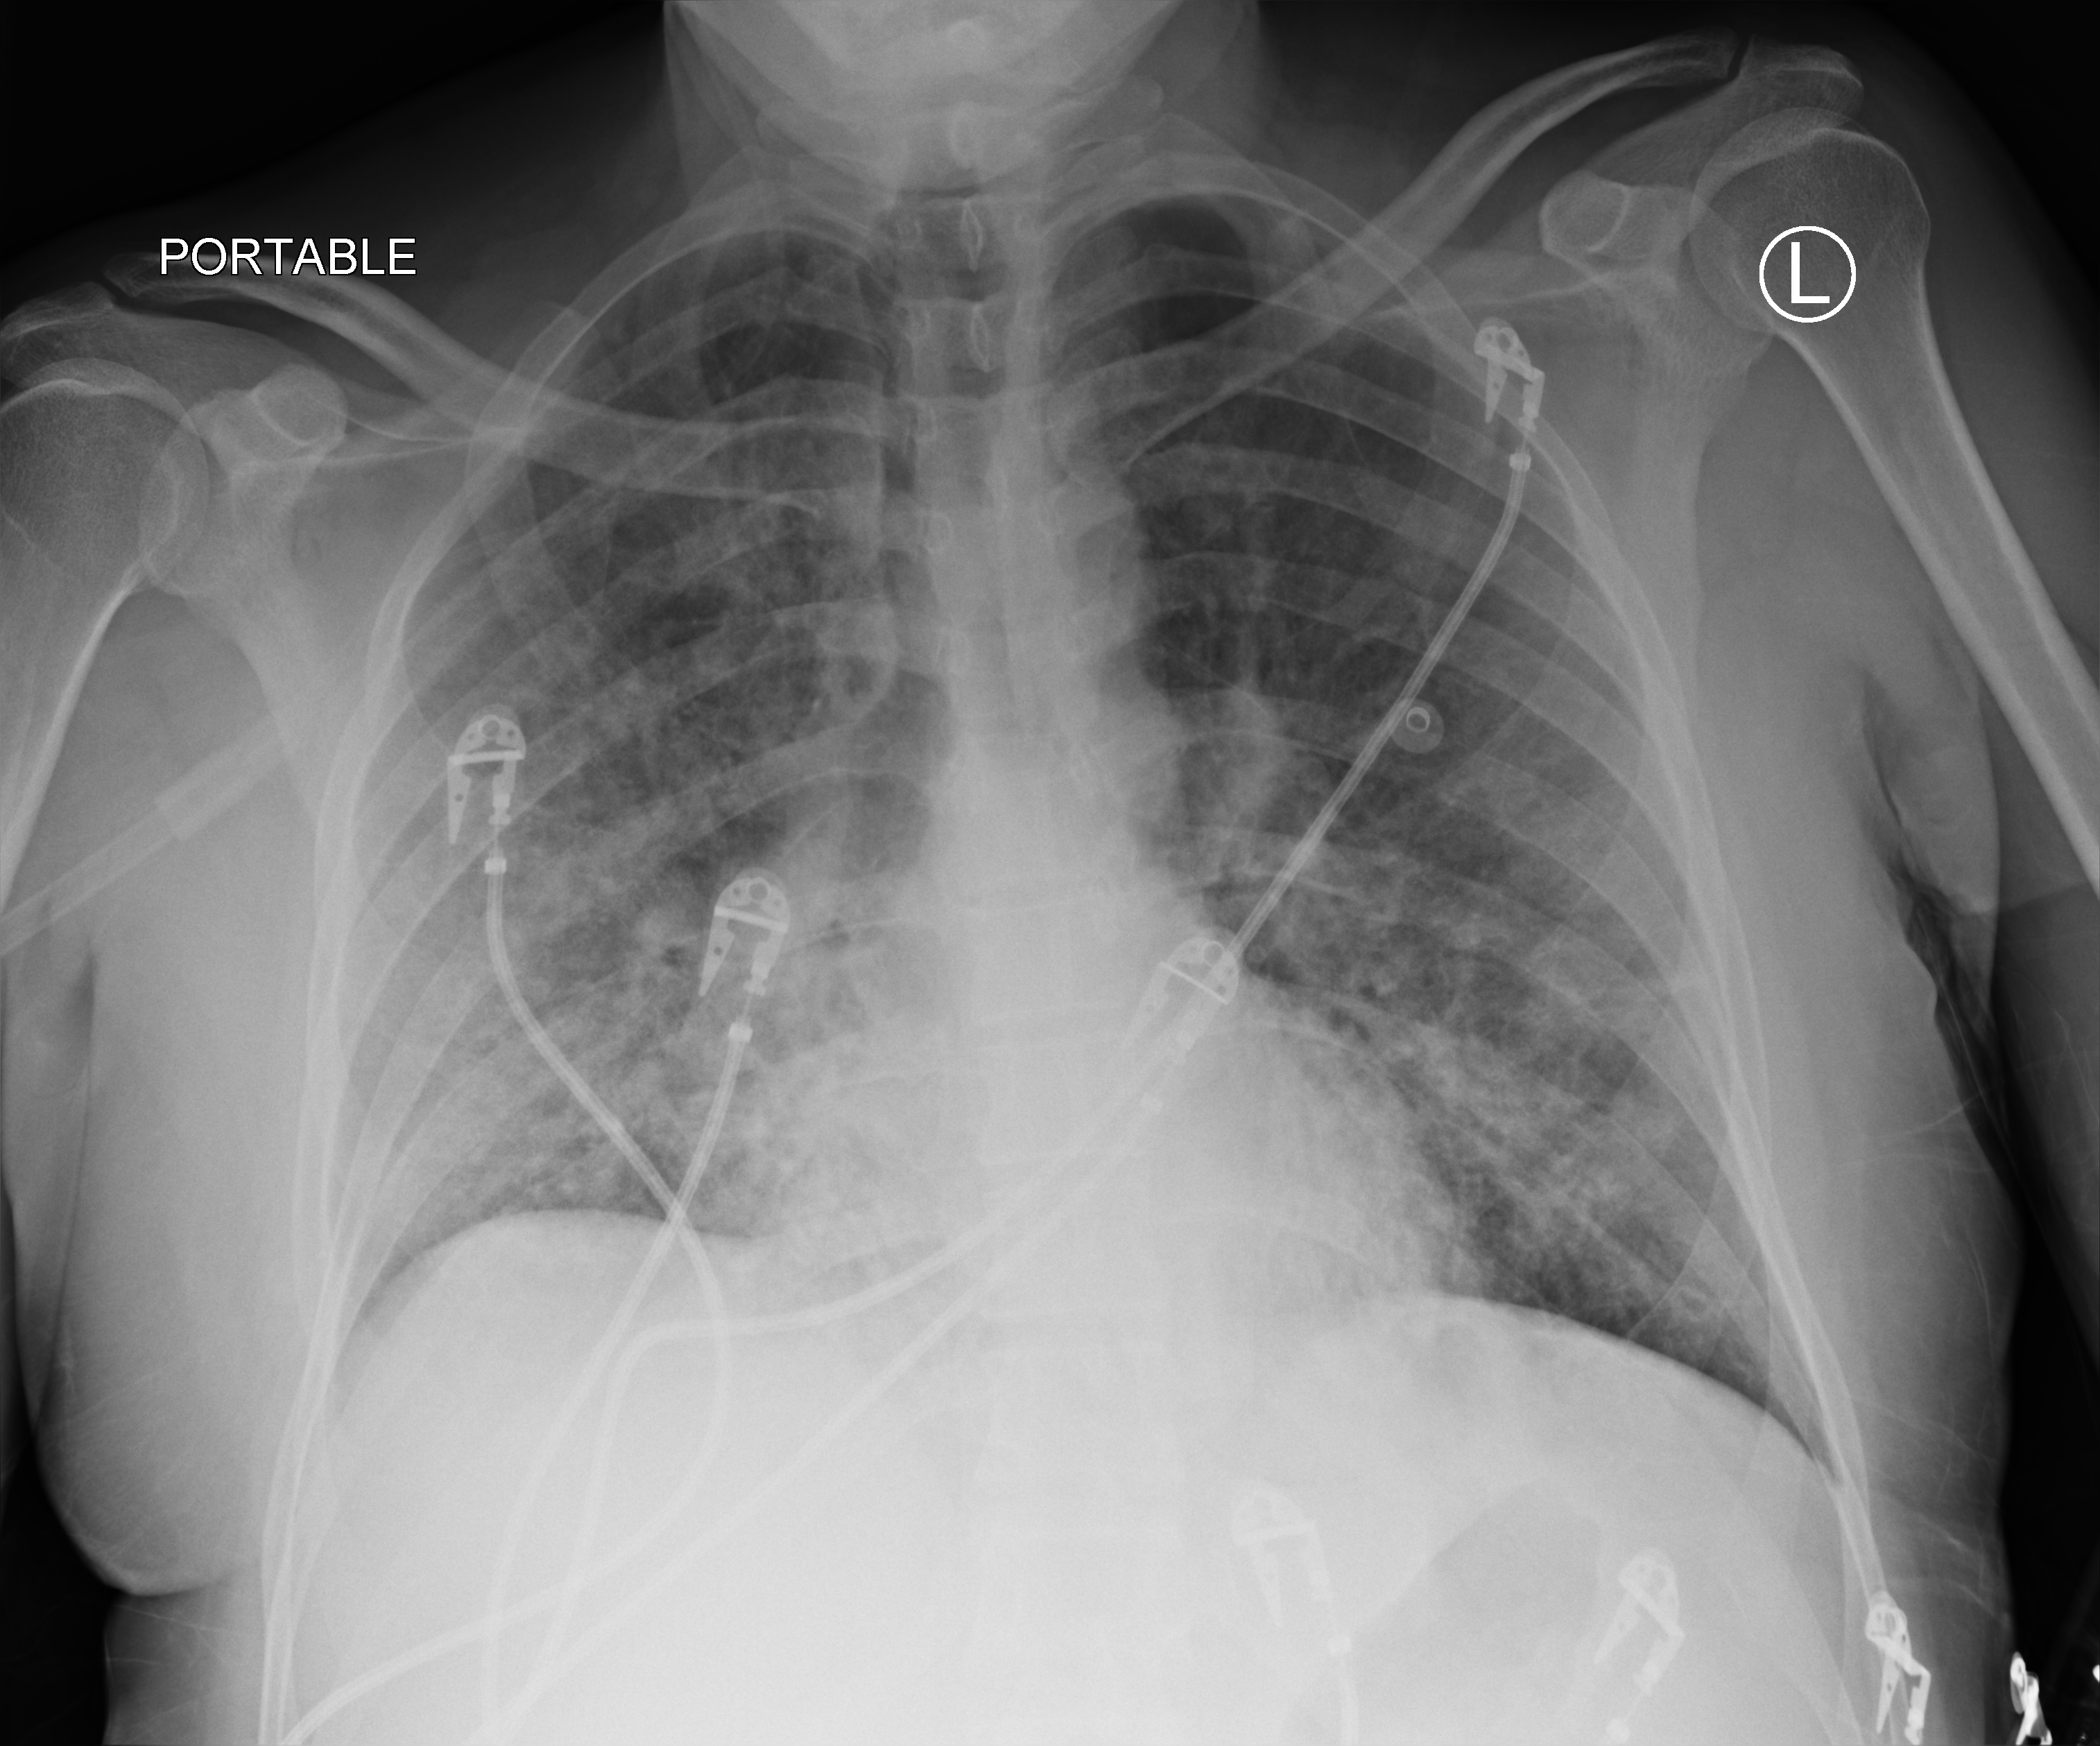
Bedside chest radiograph (computed radiography). Adult patient hospitalised with COVID-19, age 18–59 years.
Hospital-stay facts (about this admission, not read from this image; timing relative to this image not recorded): chronic kidney disease (admission record): no; mechanically ventilated during this hospital stay: yes.